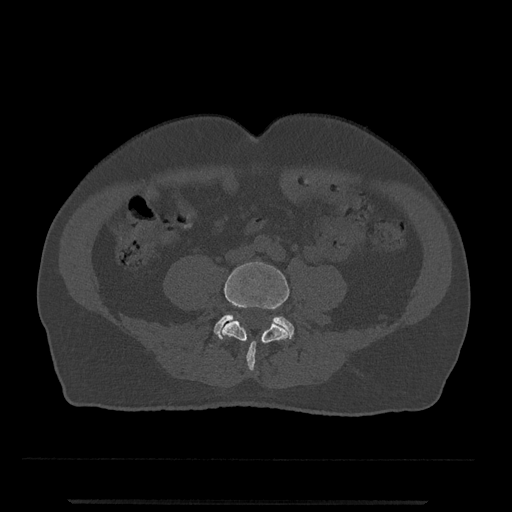
CT including the spine, one axial slice; slice 114 of 797 in the series (ordered by position); reconstruction kernel Br40s/3; bone window (W 1800 / L 400 HU); 512 × 512 image matrix, field of view 419 × 419 mm. Male patient, age 63 years. Case-level facts recorded for this patient, not image findings: primary cancer: prostate.
Annotated regions visible in this slice (semi-automatically segmented with operator editing):
- L4 vertebra: bounding box [x1, y1, x2, y2] px = [222, 262, 289, 371]
- L5 vertebra: [214, 314, 294, 339]